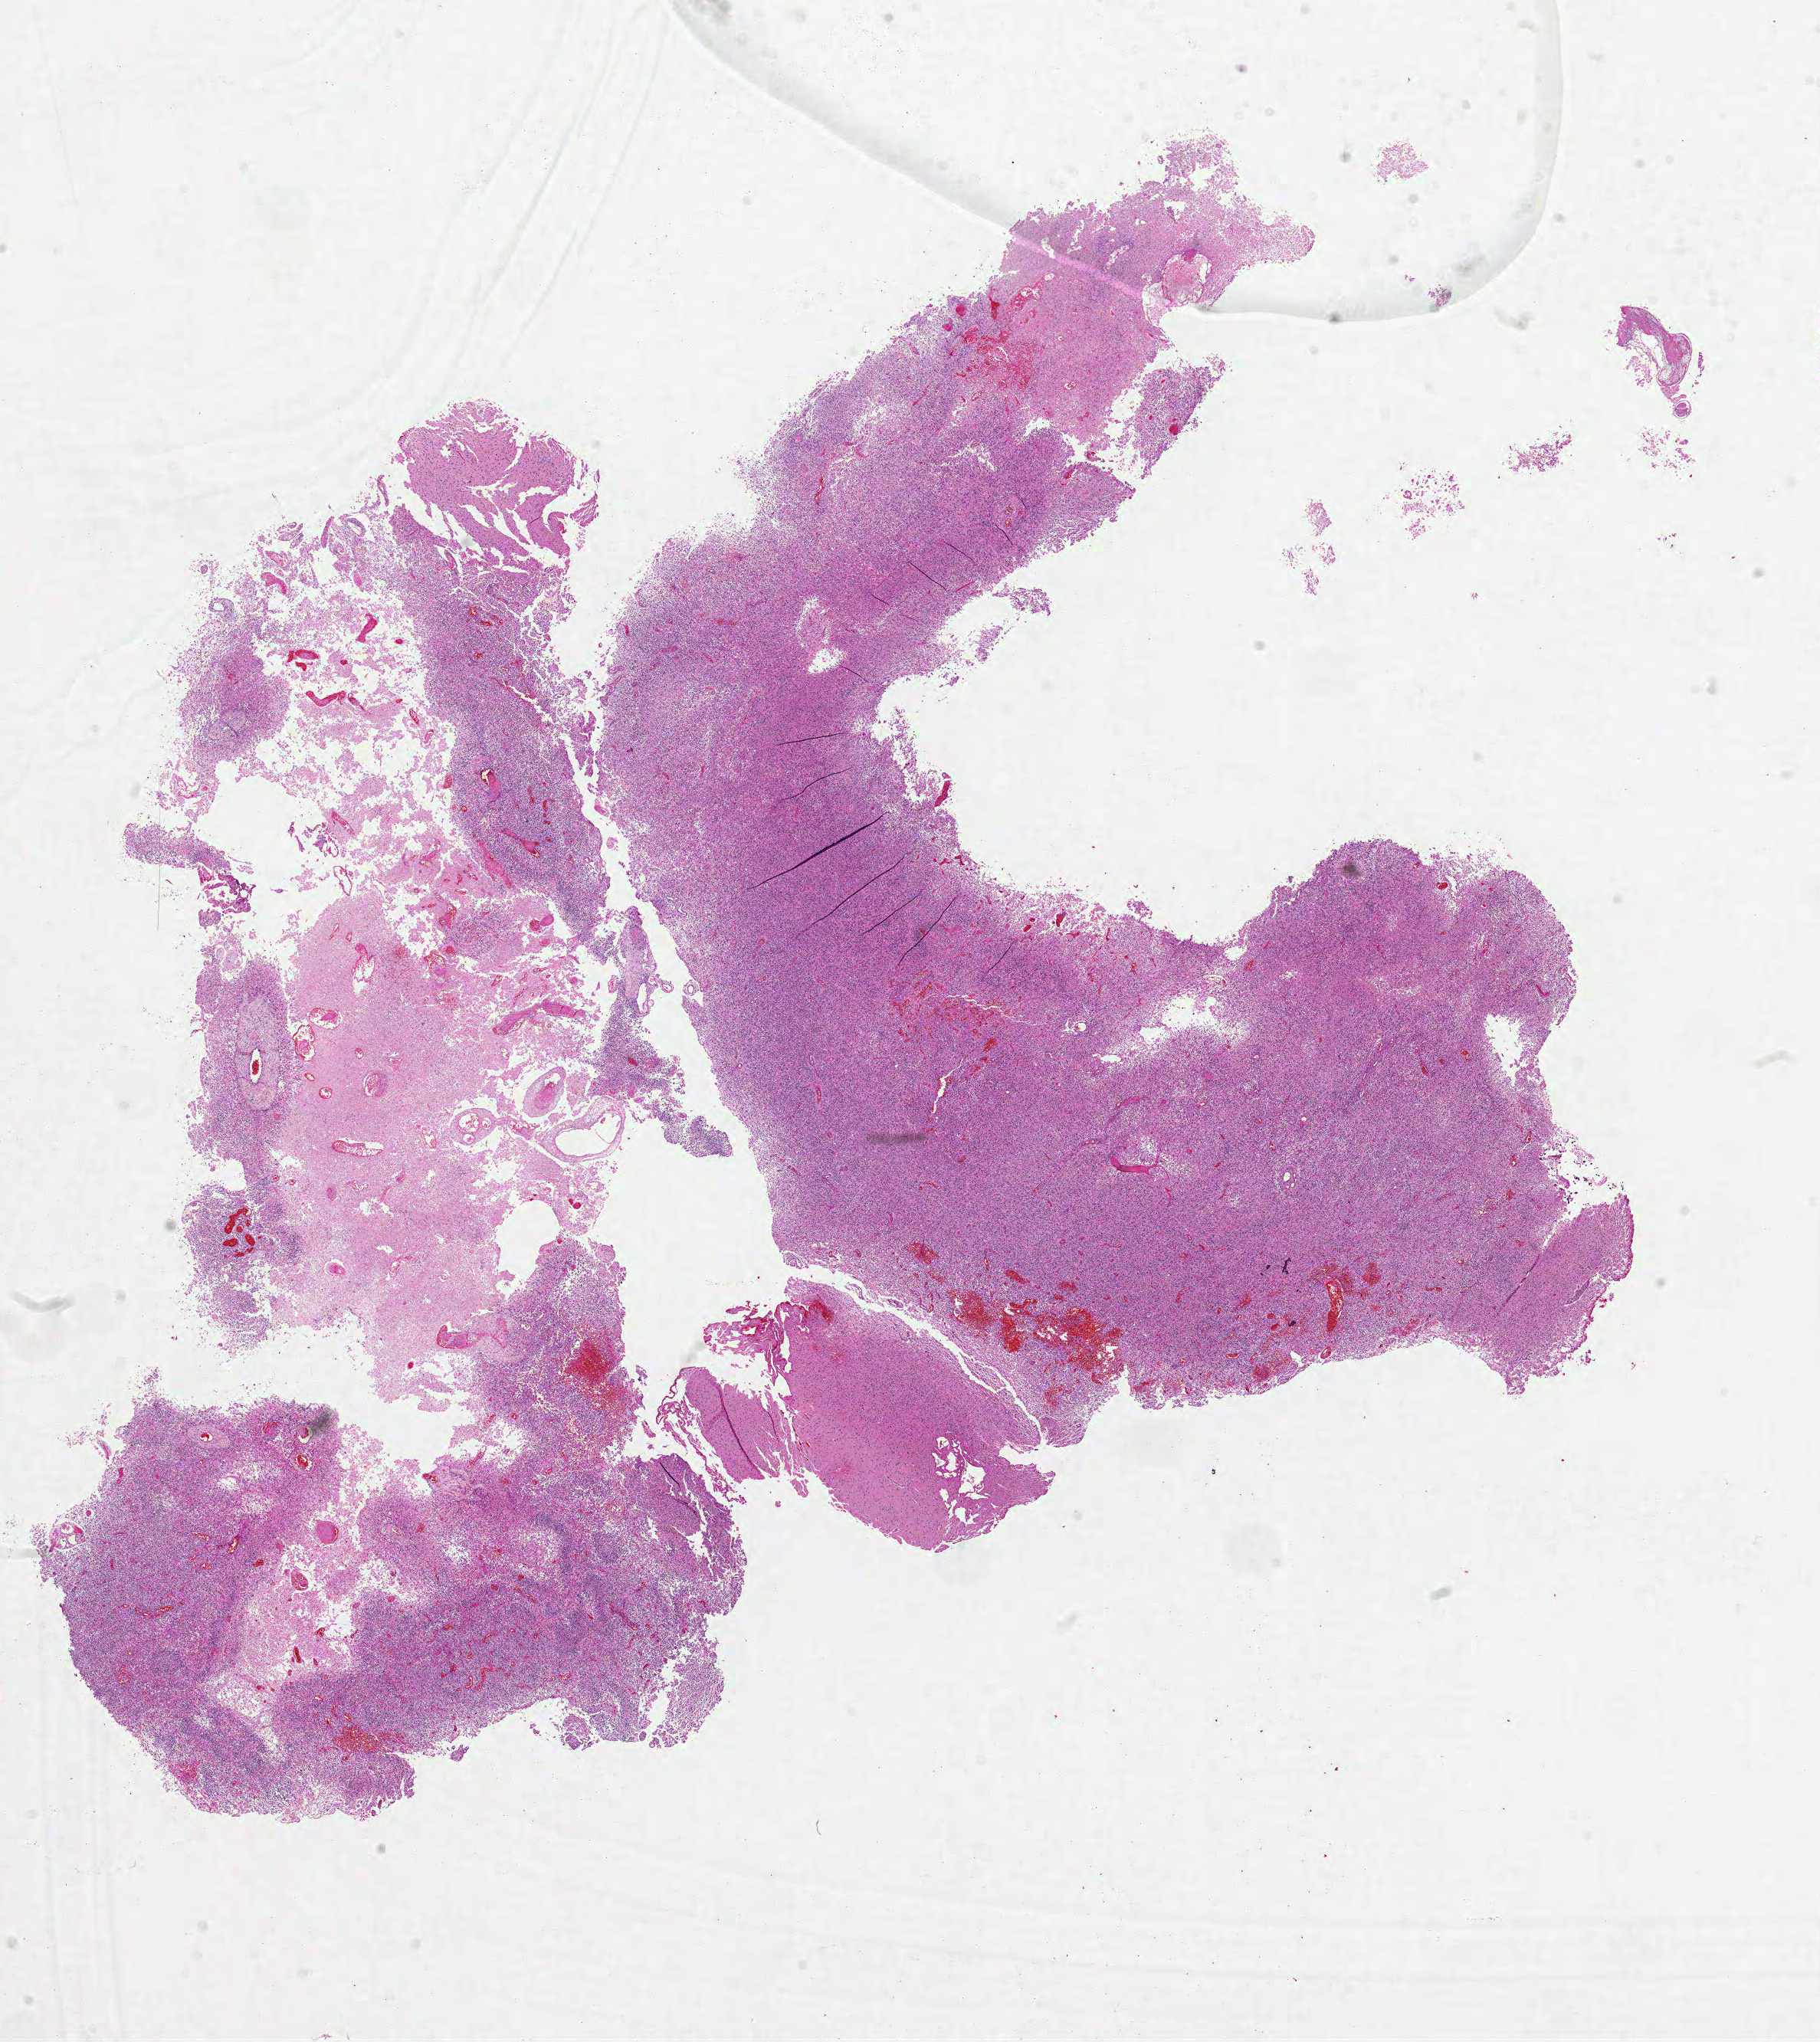
Digitized Hematoxylin and eosin (H&E) stained tissue section (whole slide), low-resolution overview of the scanned area, about 19.0 x 21.3 mm (from a 20x scan); FFPE section; brain, primary tumour sample. Male patient; age at initial diagnosis 57 years.
Diagnosis: Glioblastoma.